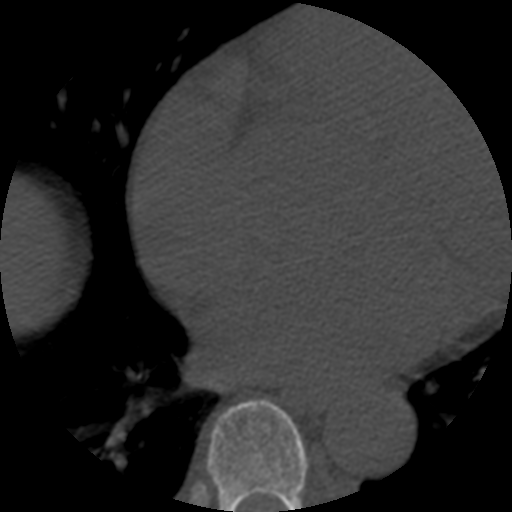
CT including the spine, one axial slice; slice 335 of 508 in the series (ordered by position); bone window (W 1800 / L 400 HU); 512 × 512 image matrix, field of view 160 × 160 mm. Patient age 57 years. Case-level facts recorded for this patient, not image findings: primary cancer: prostate.
Structures marked on this image (semi-automatic segmentation, software-assisted and operator-edited):
- T7 vertebra: bounding box <208,399,308,512> (left, top, right, bottom; pixels)